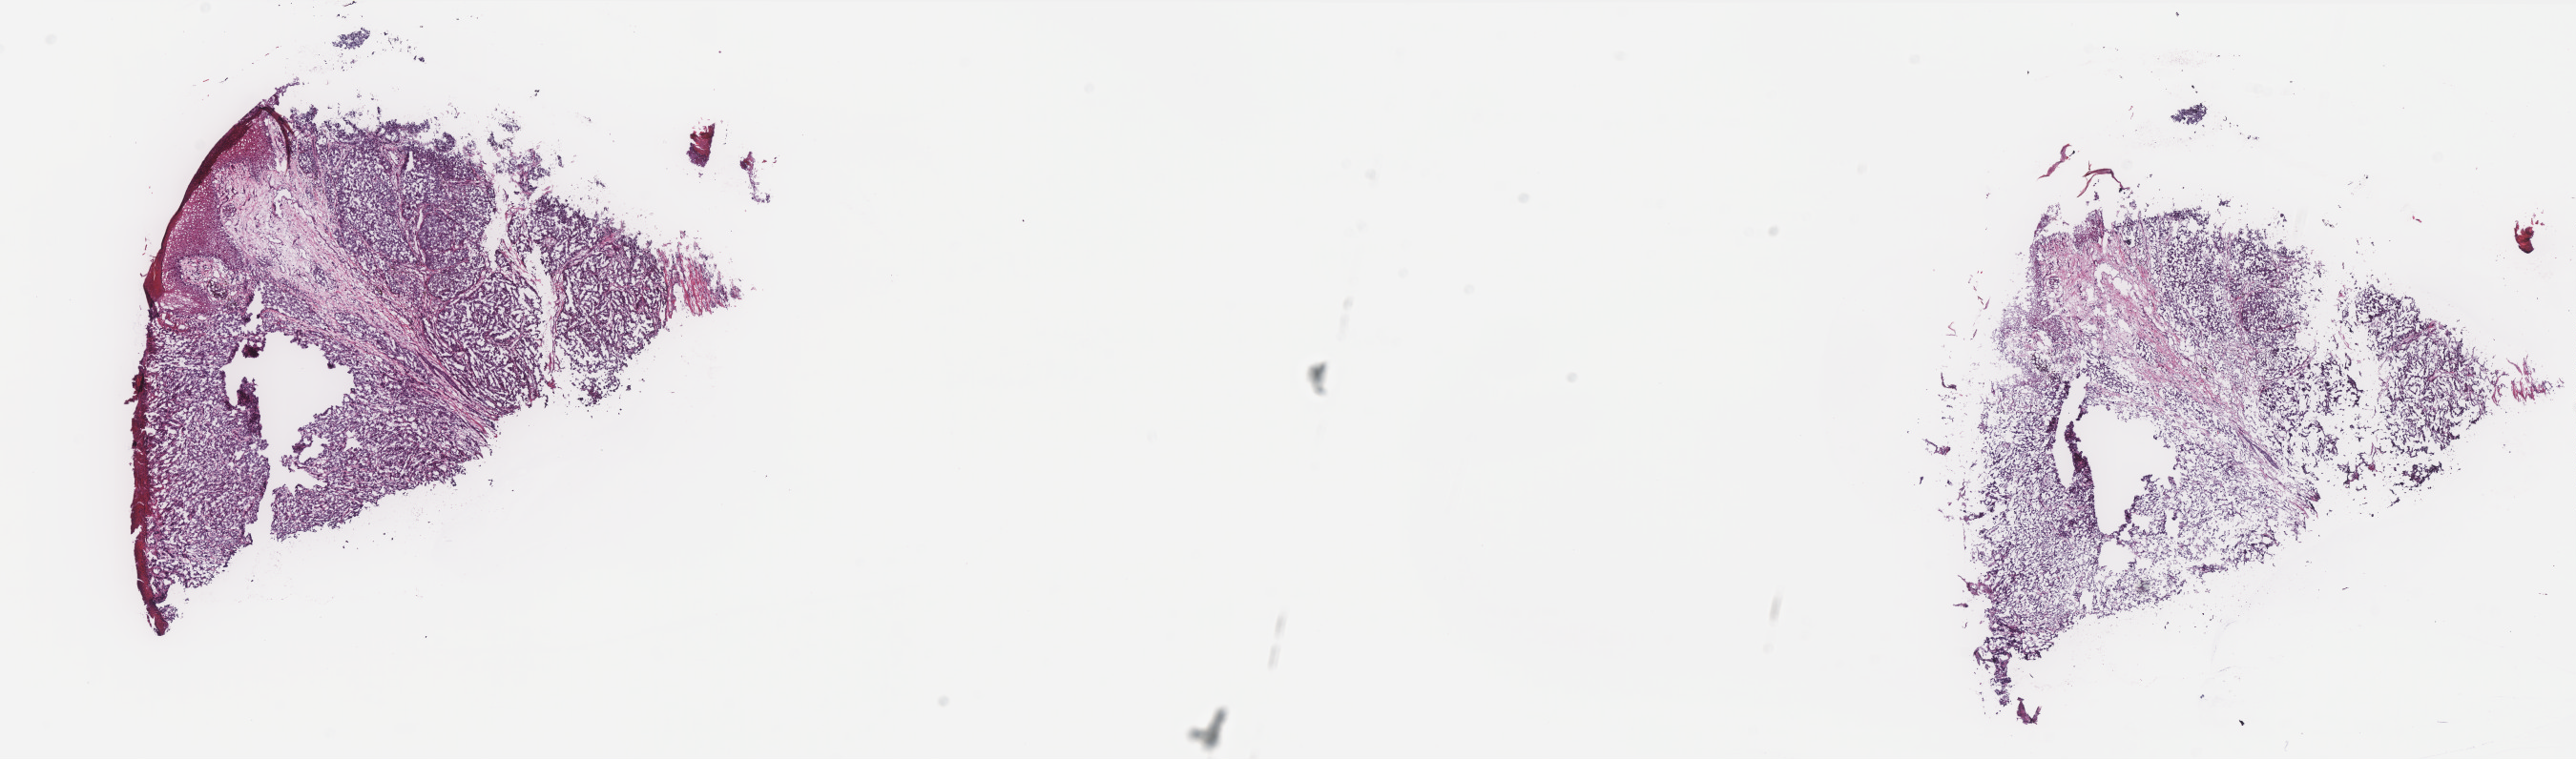
Digitized Hematoxylin and eosin (H&E) stained tissue section (whole slide), shown as a low-resolution overview of the whole scanned area (about 21.6 x 6.4 mm); frozen section from the top of the tissue portion; primary tumour sample from the skin. Male patient; age at initial diagnosis 48 years. Pathologist review of this section (percent, as recorded): tumour cells 75%, tumour nuclei 75%, normal cells 8%, stromal cells 17%, necrosis 0%. Infiltration values recorded for this section: lymphocyte infiltration 3%, monocyte infiltration 1%, neutrophil infiltration 0%.
- histologic diagnosis: Malignant melanoma, NOS
- AJCC pathologic stage: IIC (7th edition)